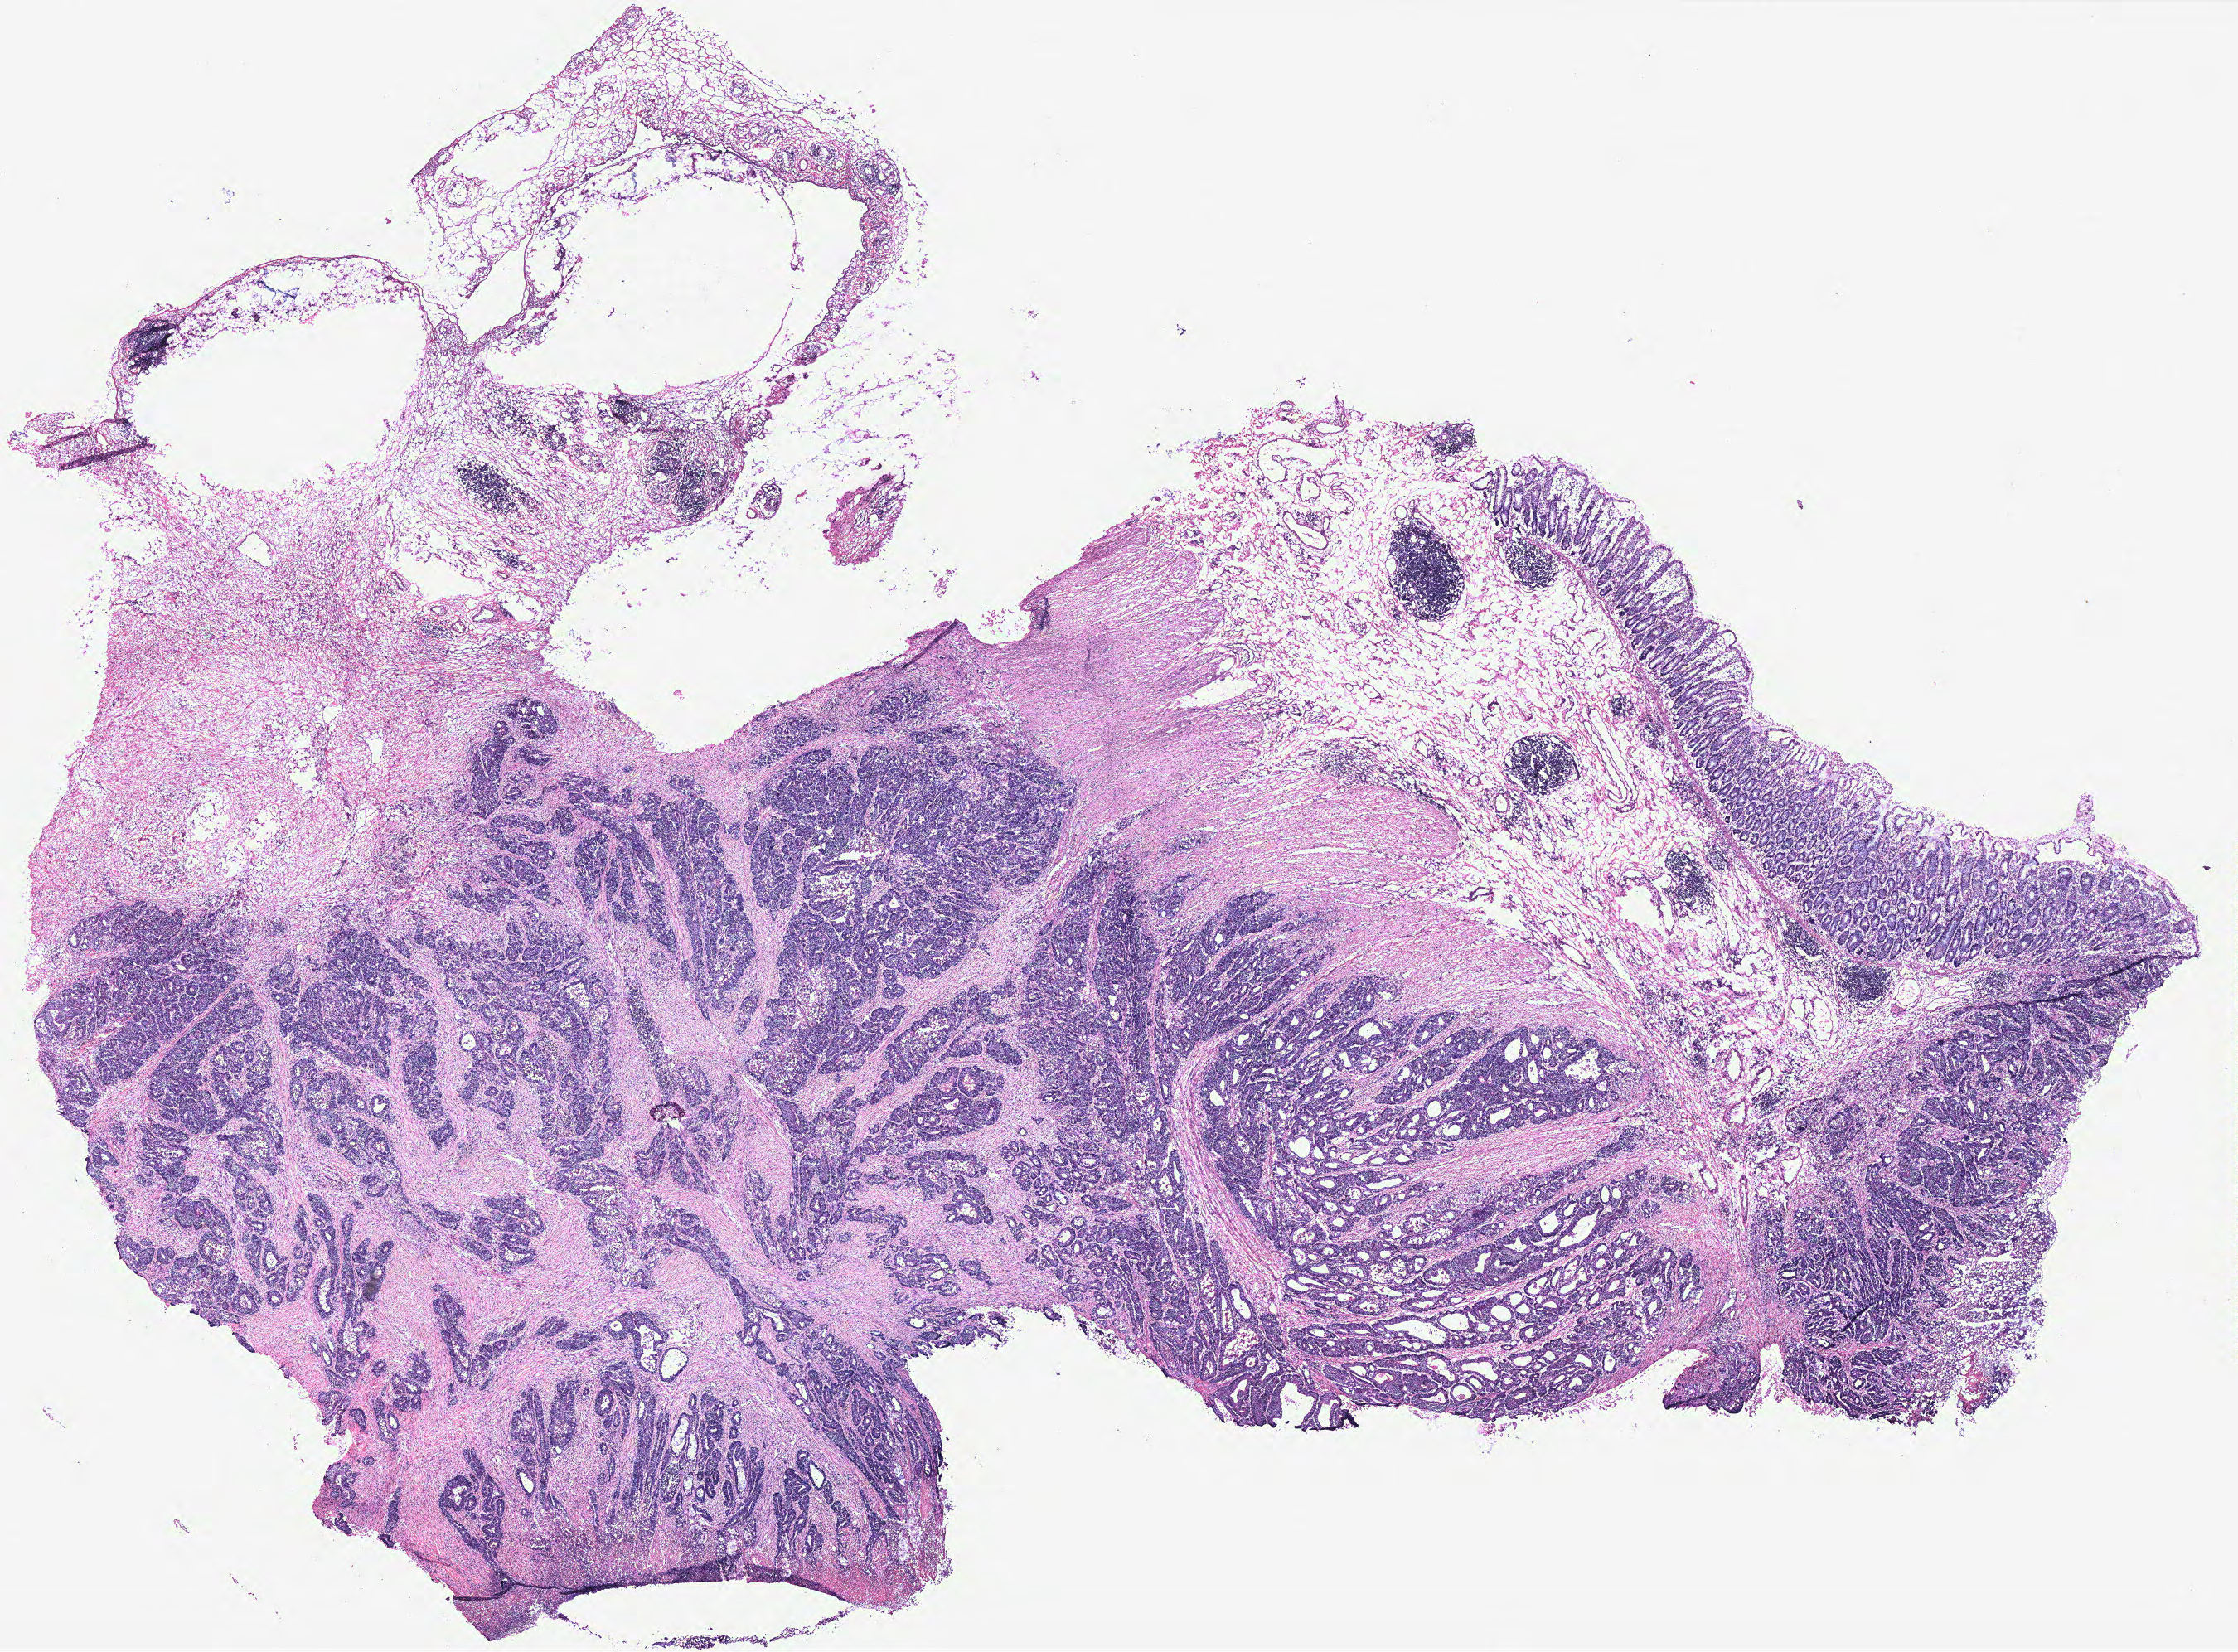
Digitized H&E-stained tissue section (whole slide), shown as a low-resolution overview of the whole scanned area (about 21.6 x 16.0 mm, acquisition: 40x scan). Colon, tissue type not recorded.
• patient diagnosis (cohort enrolment): colon cancer (colon)